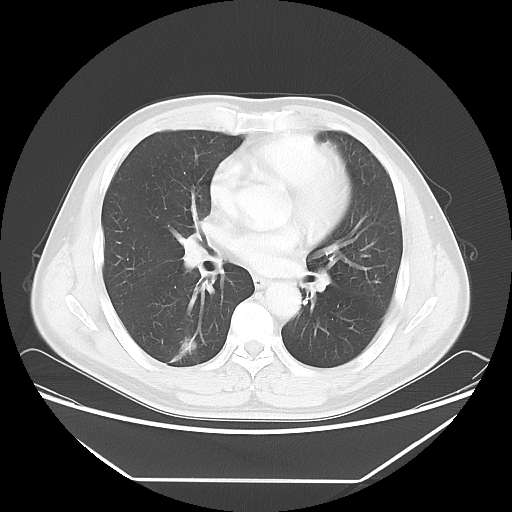
Chest CT, one axial slice; slice 33 of 65 in the series (ordered by position); reconstruction kernel LUNG; 120 kVp; lung window (W 1500 / L -600 HU); 512 × 512 image matrix, field of view 418 × 418 mm. Patient: male, 50 years. From the clinical record (not read from this slice): clinical TNM (as recorded): T1c N0 M0.
Outlined on this slice (rectangle marked by the reading radiologist):
- lung tumour (recorded histology: adenocarcinoma): box from (x=164, y=336) to (x=199, y=367) px